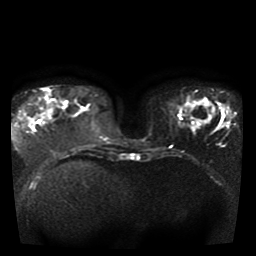
Breast MRI, one axial slice. Slice 13 of 41 in the series (ordered by position). Diffusion-weighted series; image 2 of 4 stored at this slice position (different b-values; order by instance number). 1.5 T. 5 mm slice thickness. 256 × 256 image matrix, field of view 330 × 330 mm. Female patient.
Structures marked on this image (expert manual segmentation):
- tumour on diffusion-weighted imaging: bounding box <25,116,42,126> (left, top, right, bottom; pixels)